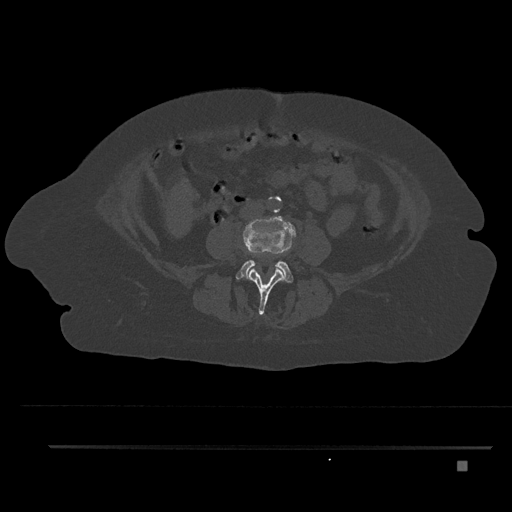
CT including the spine, one axial slice; position 102 of 797 along the scan axis; reconstruction kernel Br40s/3; bone window (W 1800 / L 400 HU); 0.5 mm slice thickness; 512 × 512 image matrix, field of view 437 × 437 mm. Patient: female, 76 years. Case-level facts recorded for this patient, not image findings: primary cancer: lung.
Structures marked on this image (semi-automatically segmented with operator editing):
- L3 vertebra: bounding box [x1, y1, x2, y2] px = [249, 219, 285, 315]
- L4 vertebra: [235, 216, 295, 283]